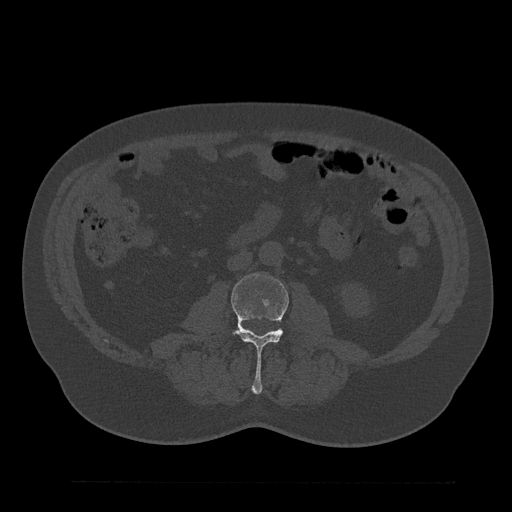
CT including the spine, one axial slice. Slice 28 of 797 in the series (ordered by position). 120 kVp. Bone window (W 1800 / L 400 HU). 512 × 512 image matrix, field of view 430 × 430 mm. Male patient, age 61 years. Case-level facts recorded for this patient, not image findings: primary cancer: prostate.
Annotated regions visible in this slice (semi-automatic segmentation, software-assisted and operator-edited):
- L3 vertebra: bounding box (x1, y1, x2, y2) in pixels: (230, 274, 289, 394)